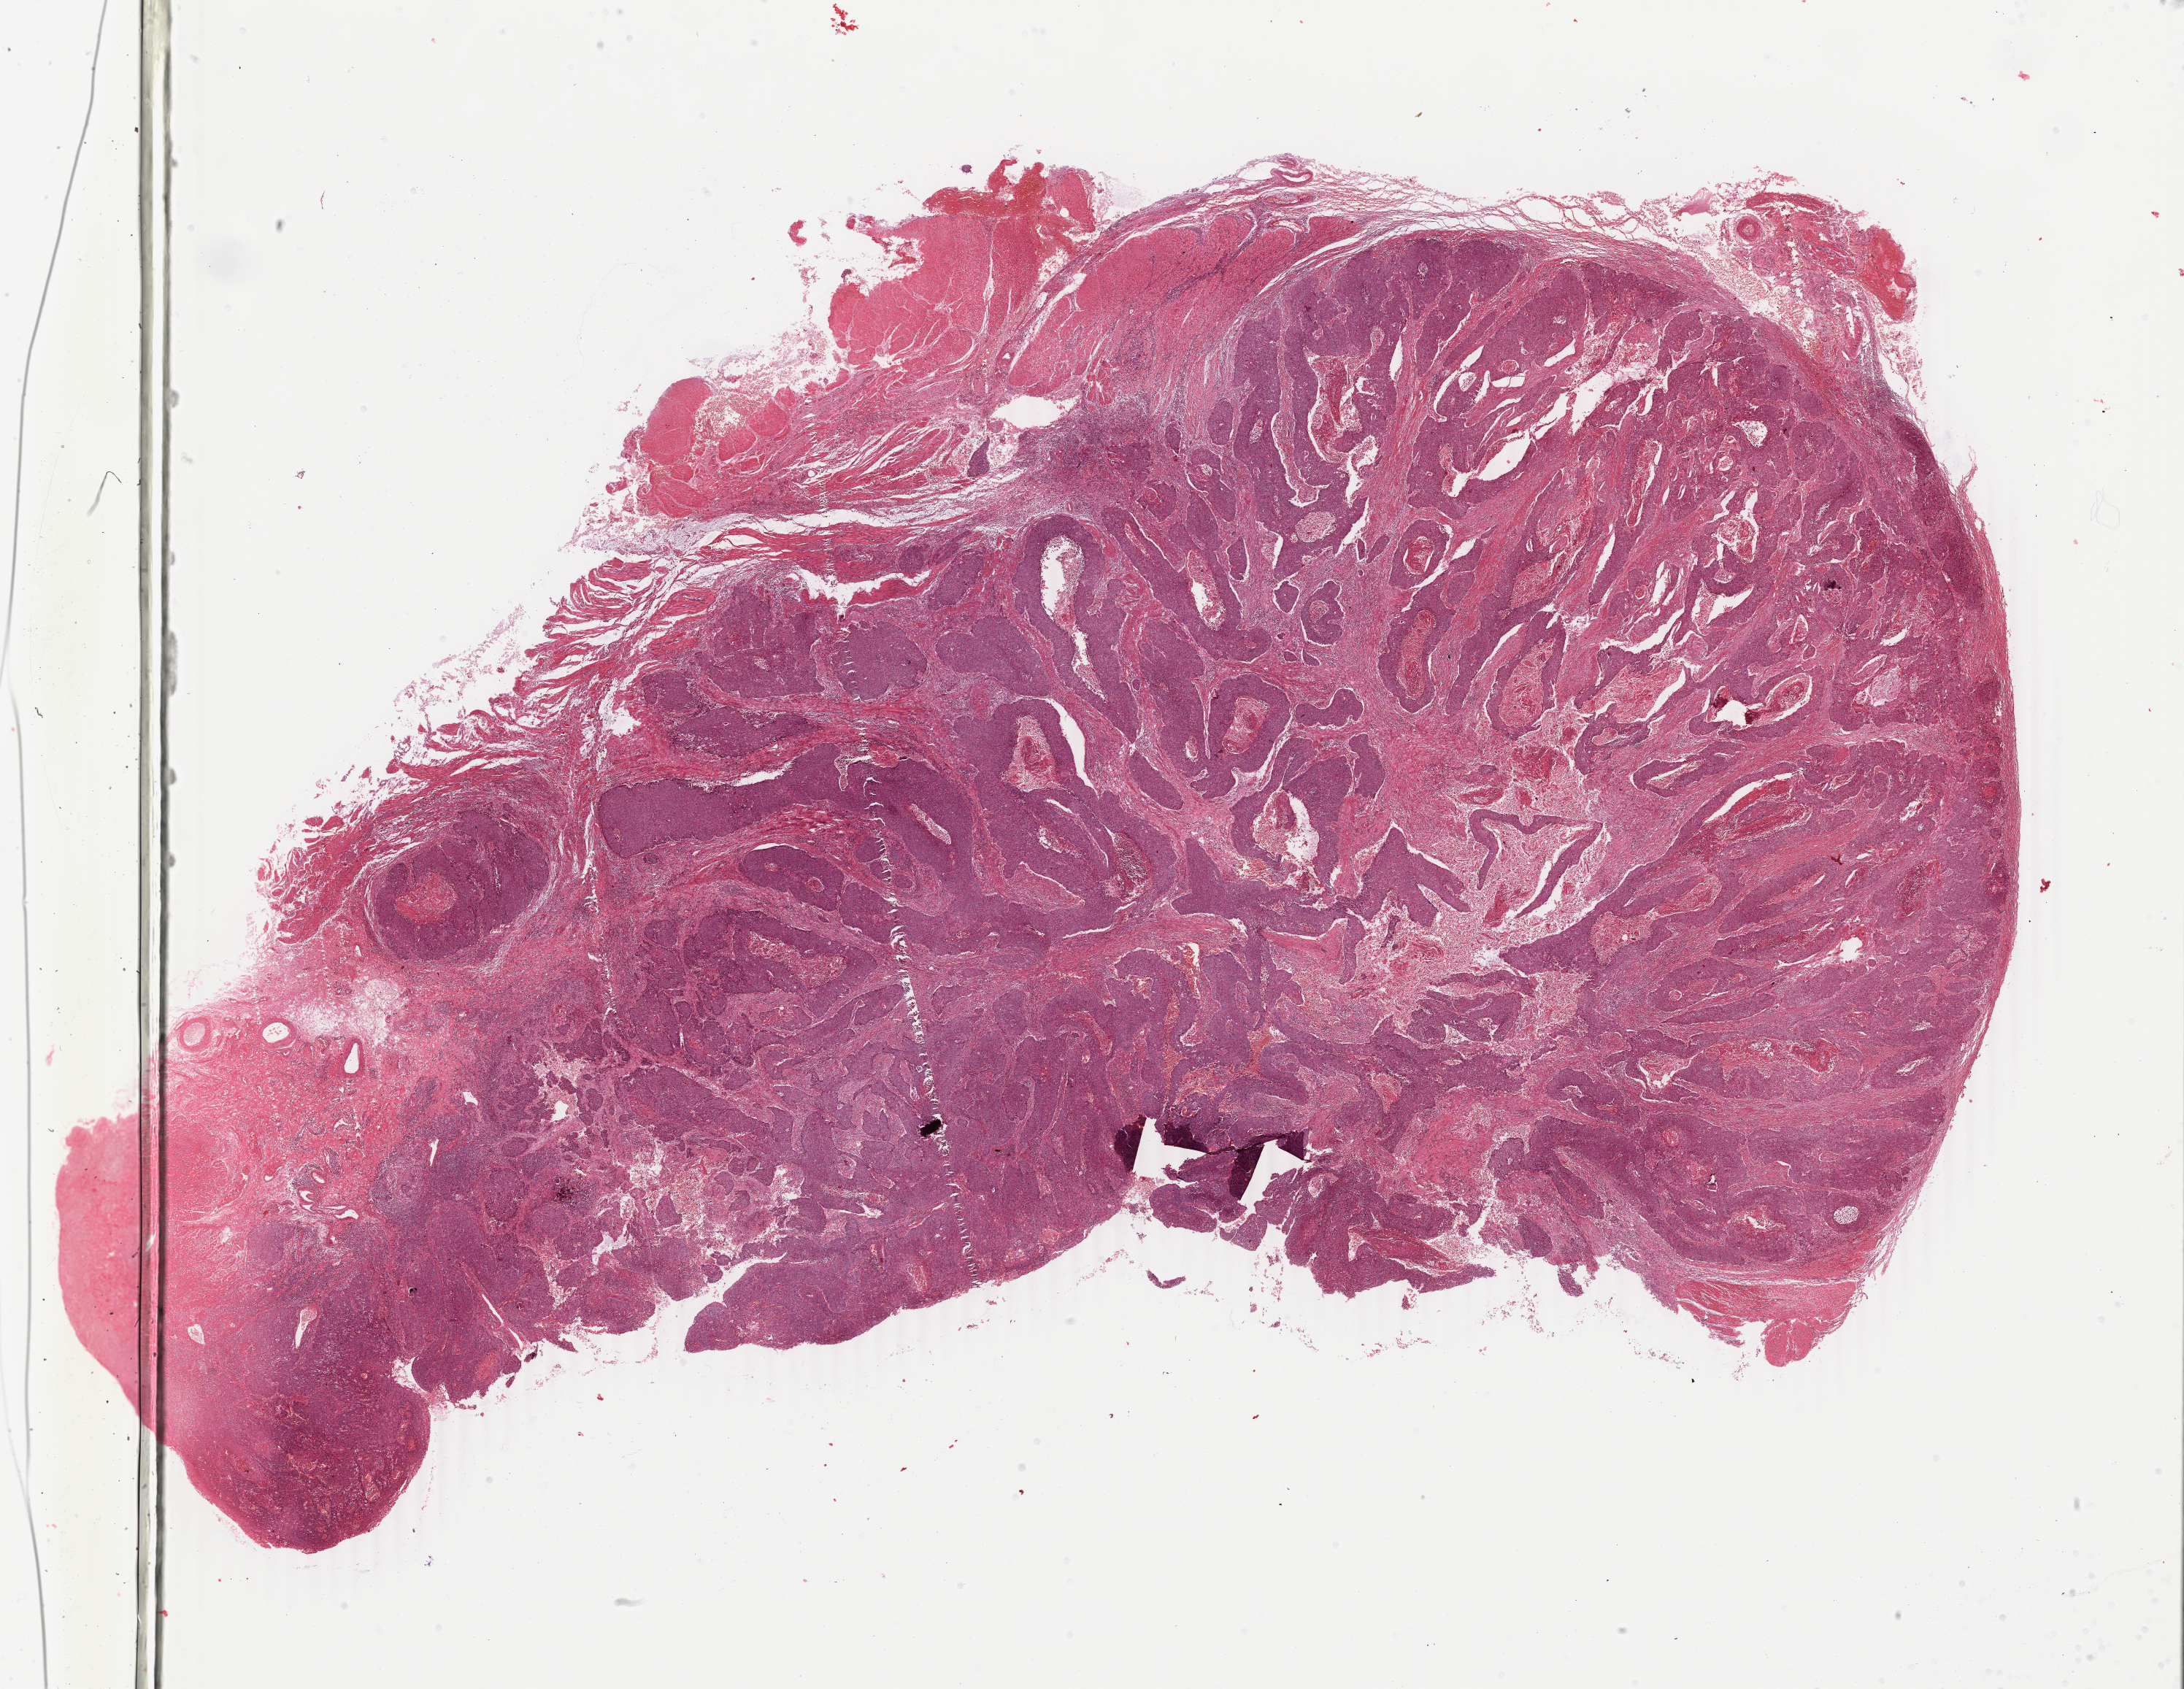
H&E whole-slide image — low-resolution overview of the scanned area, about 23.8 x 18.4 mm (acquisition: 40x scan). Formalin-fixed paraffin-embedded (FFPE) diagnostic section. Primary tumour sample from the esophagus. Male patient; age at initial diagnosis 66 years. Histologic grade: G2 (moderately differentiated).
• pathologic diagnosis: Squamous cell carcinoma, NOS (middle third of esophagus)
• AJCC pathologic stage: IIA (6th edition)